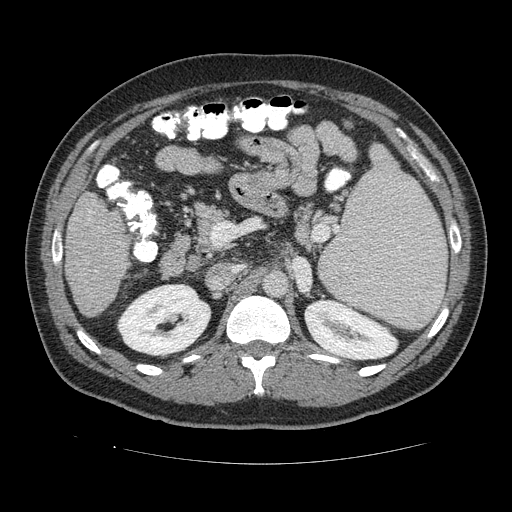
Contrast-enhanced abdominal CT (liver protocol), one axial slice. Slice 61 of 113 in the series (ordered by position). 120 kVp. Soft-tissue window (W 400 / L 40 HU). 512 × 512 image matrix, field of view 400 × 400 mm. Case-level facts recorded for this patient, not image findings: diagnosis: hepatocellular carcinoma (patient treated with transarterial chemoembolisation; whether this scan precedes or follows treatment is not stated here); TNM stage (as recorded): Stage-II; Child-Pugh class: B; tumour size: 4.8 cm.
Outlined on this slice (semi-automatic segmentation, software-assisted and operator-edited):
- liver parenchyma outside the tumour (the mass and vessels are separate outlines, so this box may not span the whole liver): box from (x=64, y=190) to (x=132, y=318) px
- liver vessels: (x=87, y=213)–(x=96, y=271)